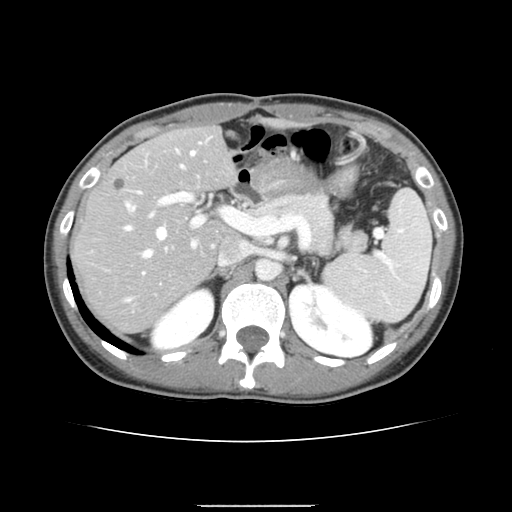
Contrast-enhanced abdominal CT, one axial slice. Slice 93 of 150 in the series (ordered by position). 120 kVp. Intravenous contrast given. Soft-tissue window (W 400 / L 40 HU). 2.5 mm slice thickness. 512 × 512 image matrix, field of view 324 × 324 mm. Female patient, age 32 years. From the clinical record (not read from this slice): diagnosis: colorectal cancer liver metastases, imaged before liver resection; multiple liver metastases: yes; largest metastasis: 0.7 cm; disease in both lobes: no.
Annotated regions visible in this slice (manually delineated by an expert):
- hepatic veins: box from (x=126, y=151) to (x=195, y=300) px
- liver: (x=74, y=128)–(x=236, y=333)
- planned liver remnant (the part of the liver to remain after resection): (x=74, y=128)–(x=236, y=279)
- portal vein (with intrahepatic branches): (x=135, y=190)–(x=234, y=273)
- liver metastasis: (x=115, y=181)–(x=125, y=191)